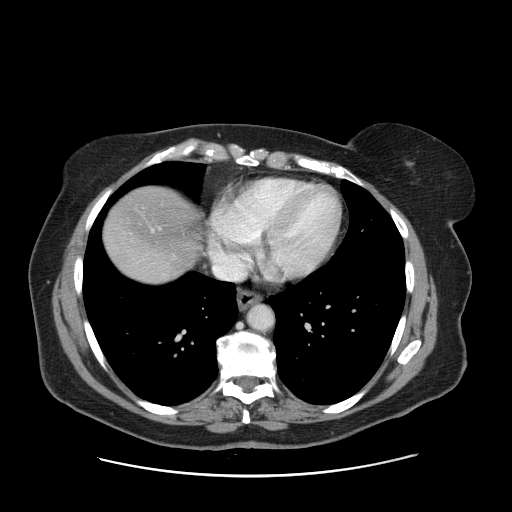
Contrast-enhanced abdominal CT, one axial slice; slice 146 of 161 in the series (ordered by position); 120 kVp; intravenous contrast given; soft-tissue window (W 400 / L 40 HU); 512 × 512 image matrix, field of view 398 × 398 mm. Female patient, age 62 years. Case-level facts recorded for this patient, not image findings: diagnosis: colorectal cancer liver metastases, imaged before liver resection; multiple liver metastases: no; largest metastasis: 2.5 cm.
Outlined on this slice (outlined manually by an expert reader):
- liver: bounding box <104,187,202,281> (left, top, right, bottom; pixels)
- planned liver remnant (the part of the liver to remain after resection): <106,188,201,269>